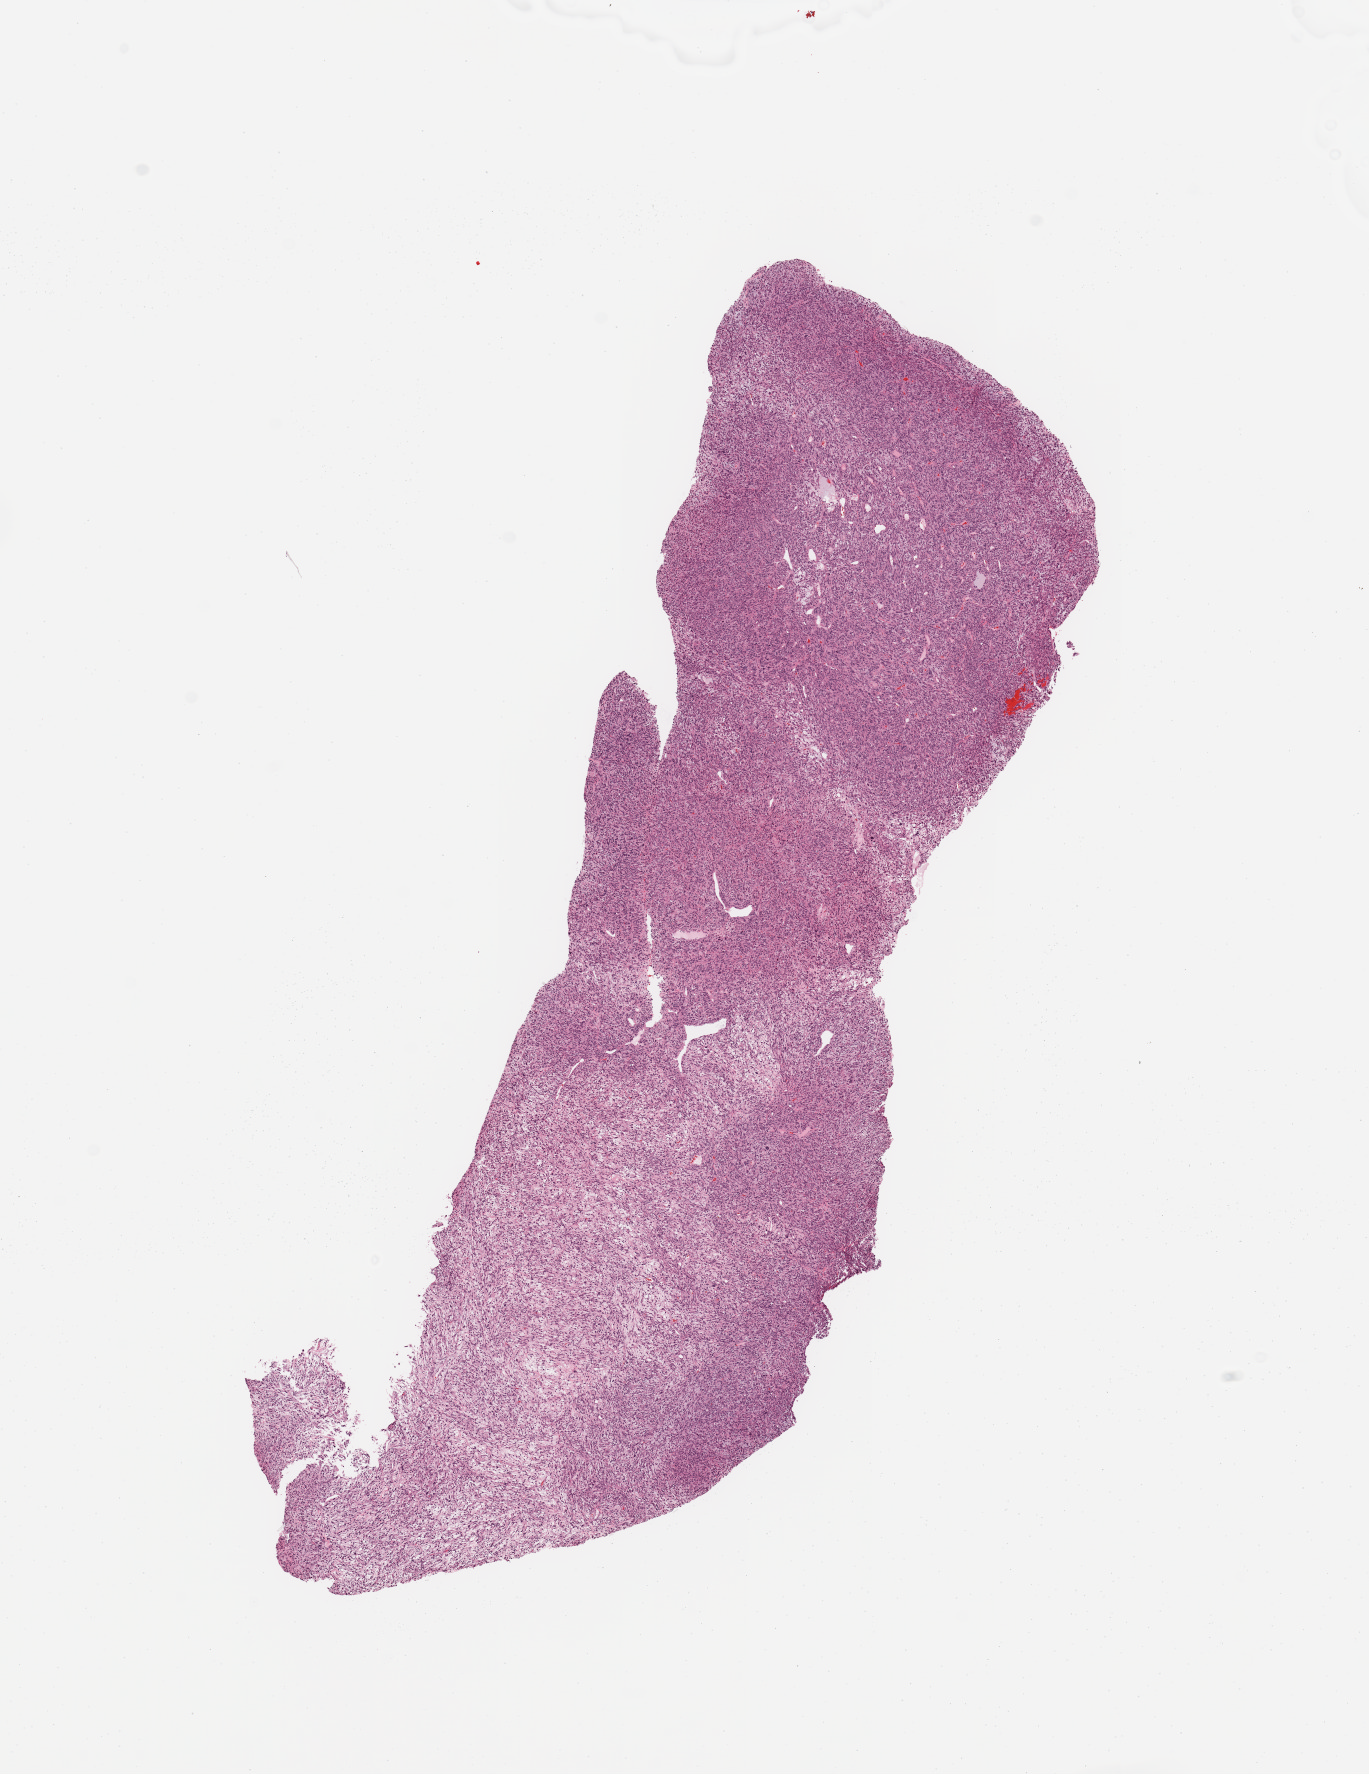
Whole-slide histology image, Hematoxylin and eosin (H&E) stained, shown as a low-resolution overview of the whole scanned area (about 10.8 x 14.0 mm, from a 20x scan). Patient: male, age 68 years.
- patient diagnosis (cohort enrolment): sarcoma (site not recorded at cohort level)